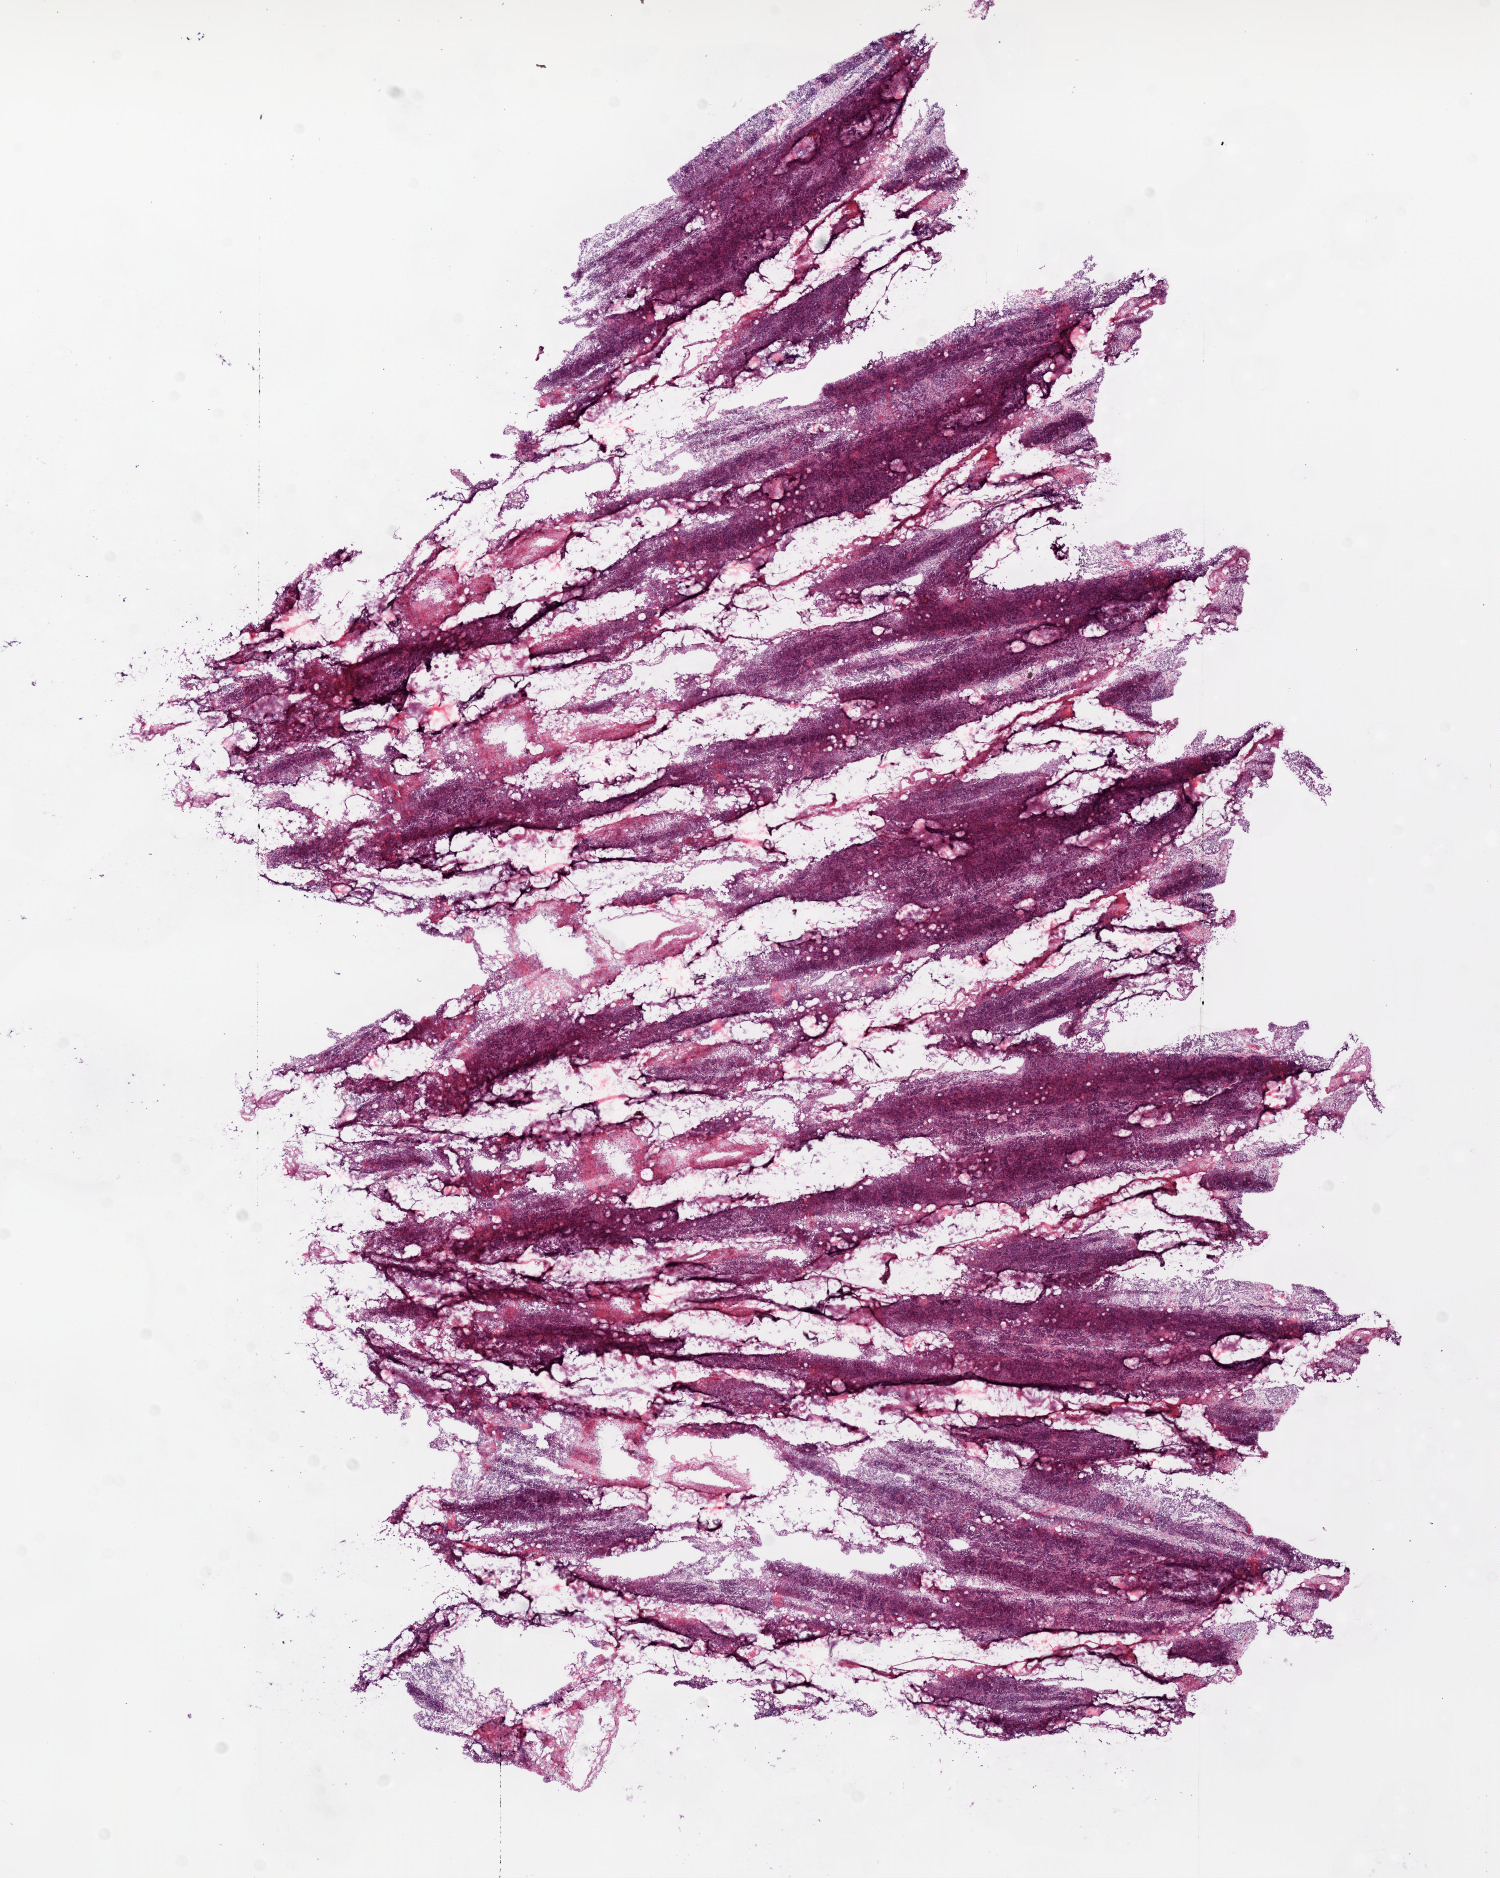
H&E-stained whole-slide image — whole scanned area (about 12.0 x 15.1 mm, acquisition: 20x scan) shown as a low-resolution overview, frozen section, ovary, primary tumour sample. Patient: female, age at initial diagnosis 80 years. Histologic grade: G3 (poorly differentiated). Composition of this section per pathologist review: tumour cells 85%, tumour nuclei 80%, normal cells 0%, stromal cells 15%, necrosis 0%.
FIGO stage: IIIC. Laterality: bilateral. Pathologic diagnosis: Serous cystadenocarcinoma, NOS.